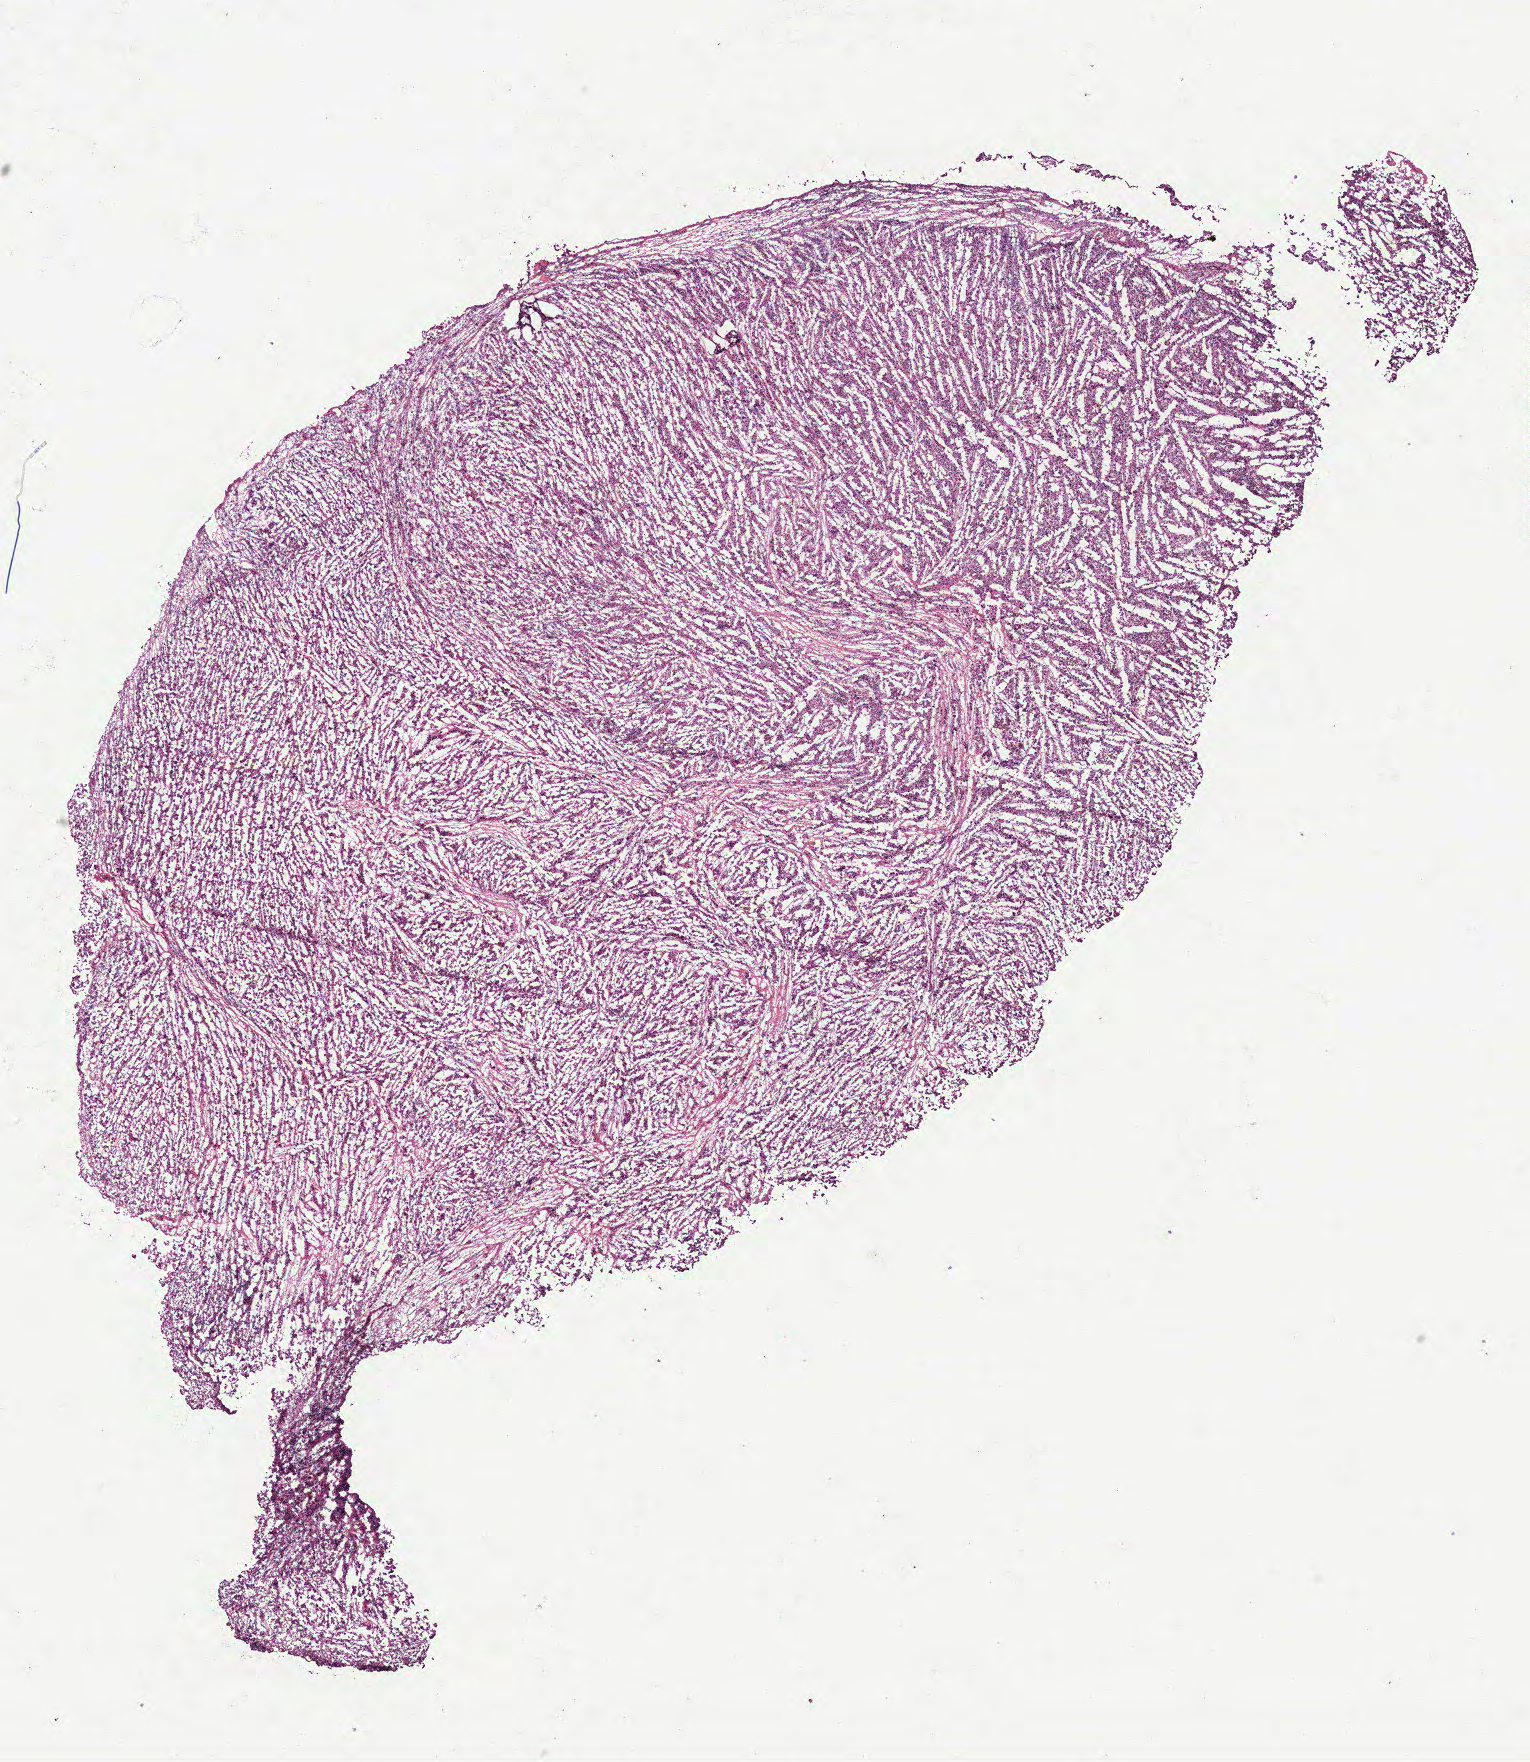
Digitized H&E-stained tissue section (whole slide), a low-resolution overview of the entire scanned area, about 12.2 x 14.1 mm. Ovary, tumour tissue. Female, 57 y/o.
Histologic diagnosis: Serous adenocarcinoma, NOS. Primary tumour site (as recorded): ovary.